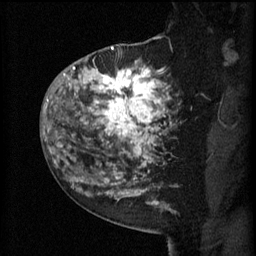
Breast MRI (dynamic contrast-enhanced), one sagittal slice; slice 40 of 60 in the series (ordered by position); 3 images stored at this slice position (order not interpretable as contrast timing); 1.5 T; TE 4.2 ms, TR 11 ms; 2 mm slice thickness; 256 × 256 image matrix, field of view 180 × 180 mm. Female patient, age 52 years.
Structures marked on this image (semi-automatic segmentation, software-assisted and operator-edited):
- analysis volume of interest (the breast-tissue region the enhancement analysis was run in; not a lesion): bounding box <81,52,174,157> (left, top, right, bottom; pixels)
- tumour enhancement mask (voxels above the 70 % enhancement threshold inside the analysis volume of interest): <81,62,171,157>